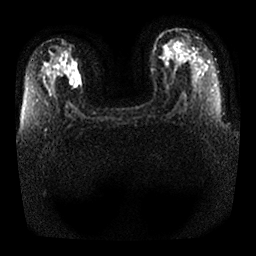
Breast MRI, one axial slice; diffusion-weighted series; image 2 of 4 stored at this slice position (different b-values; order by instance number); 1.5 T; 4 mm slice thickness; 256 × 256 image matrix, field of view 350 × 350 mm. Female patient.
Outlined on this slice (outlined manually by an expert reader):
- tumour on diffusion-weighted imaging: bounding box (x1, y1, x2, y2) in pixels: (70, 72, 81, 82)